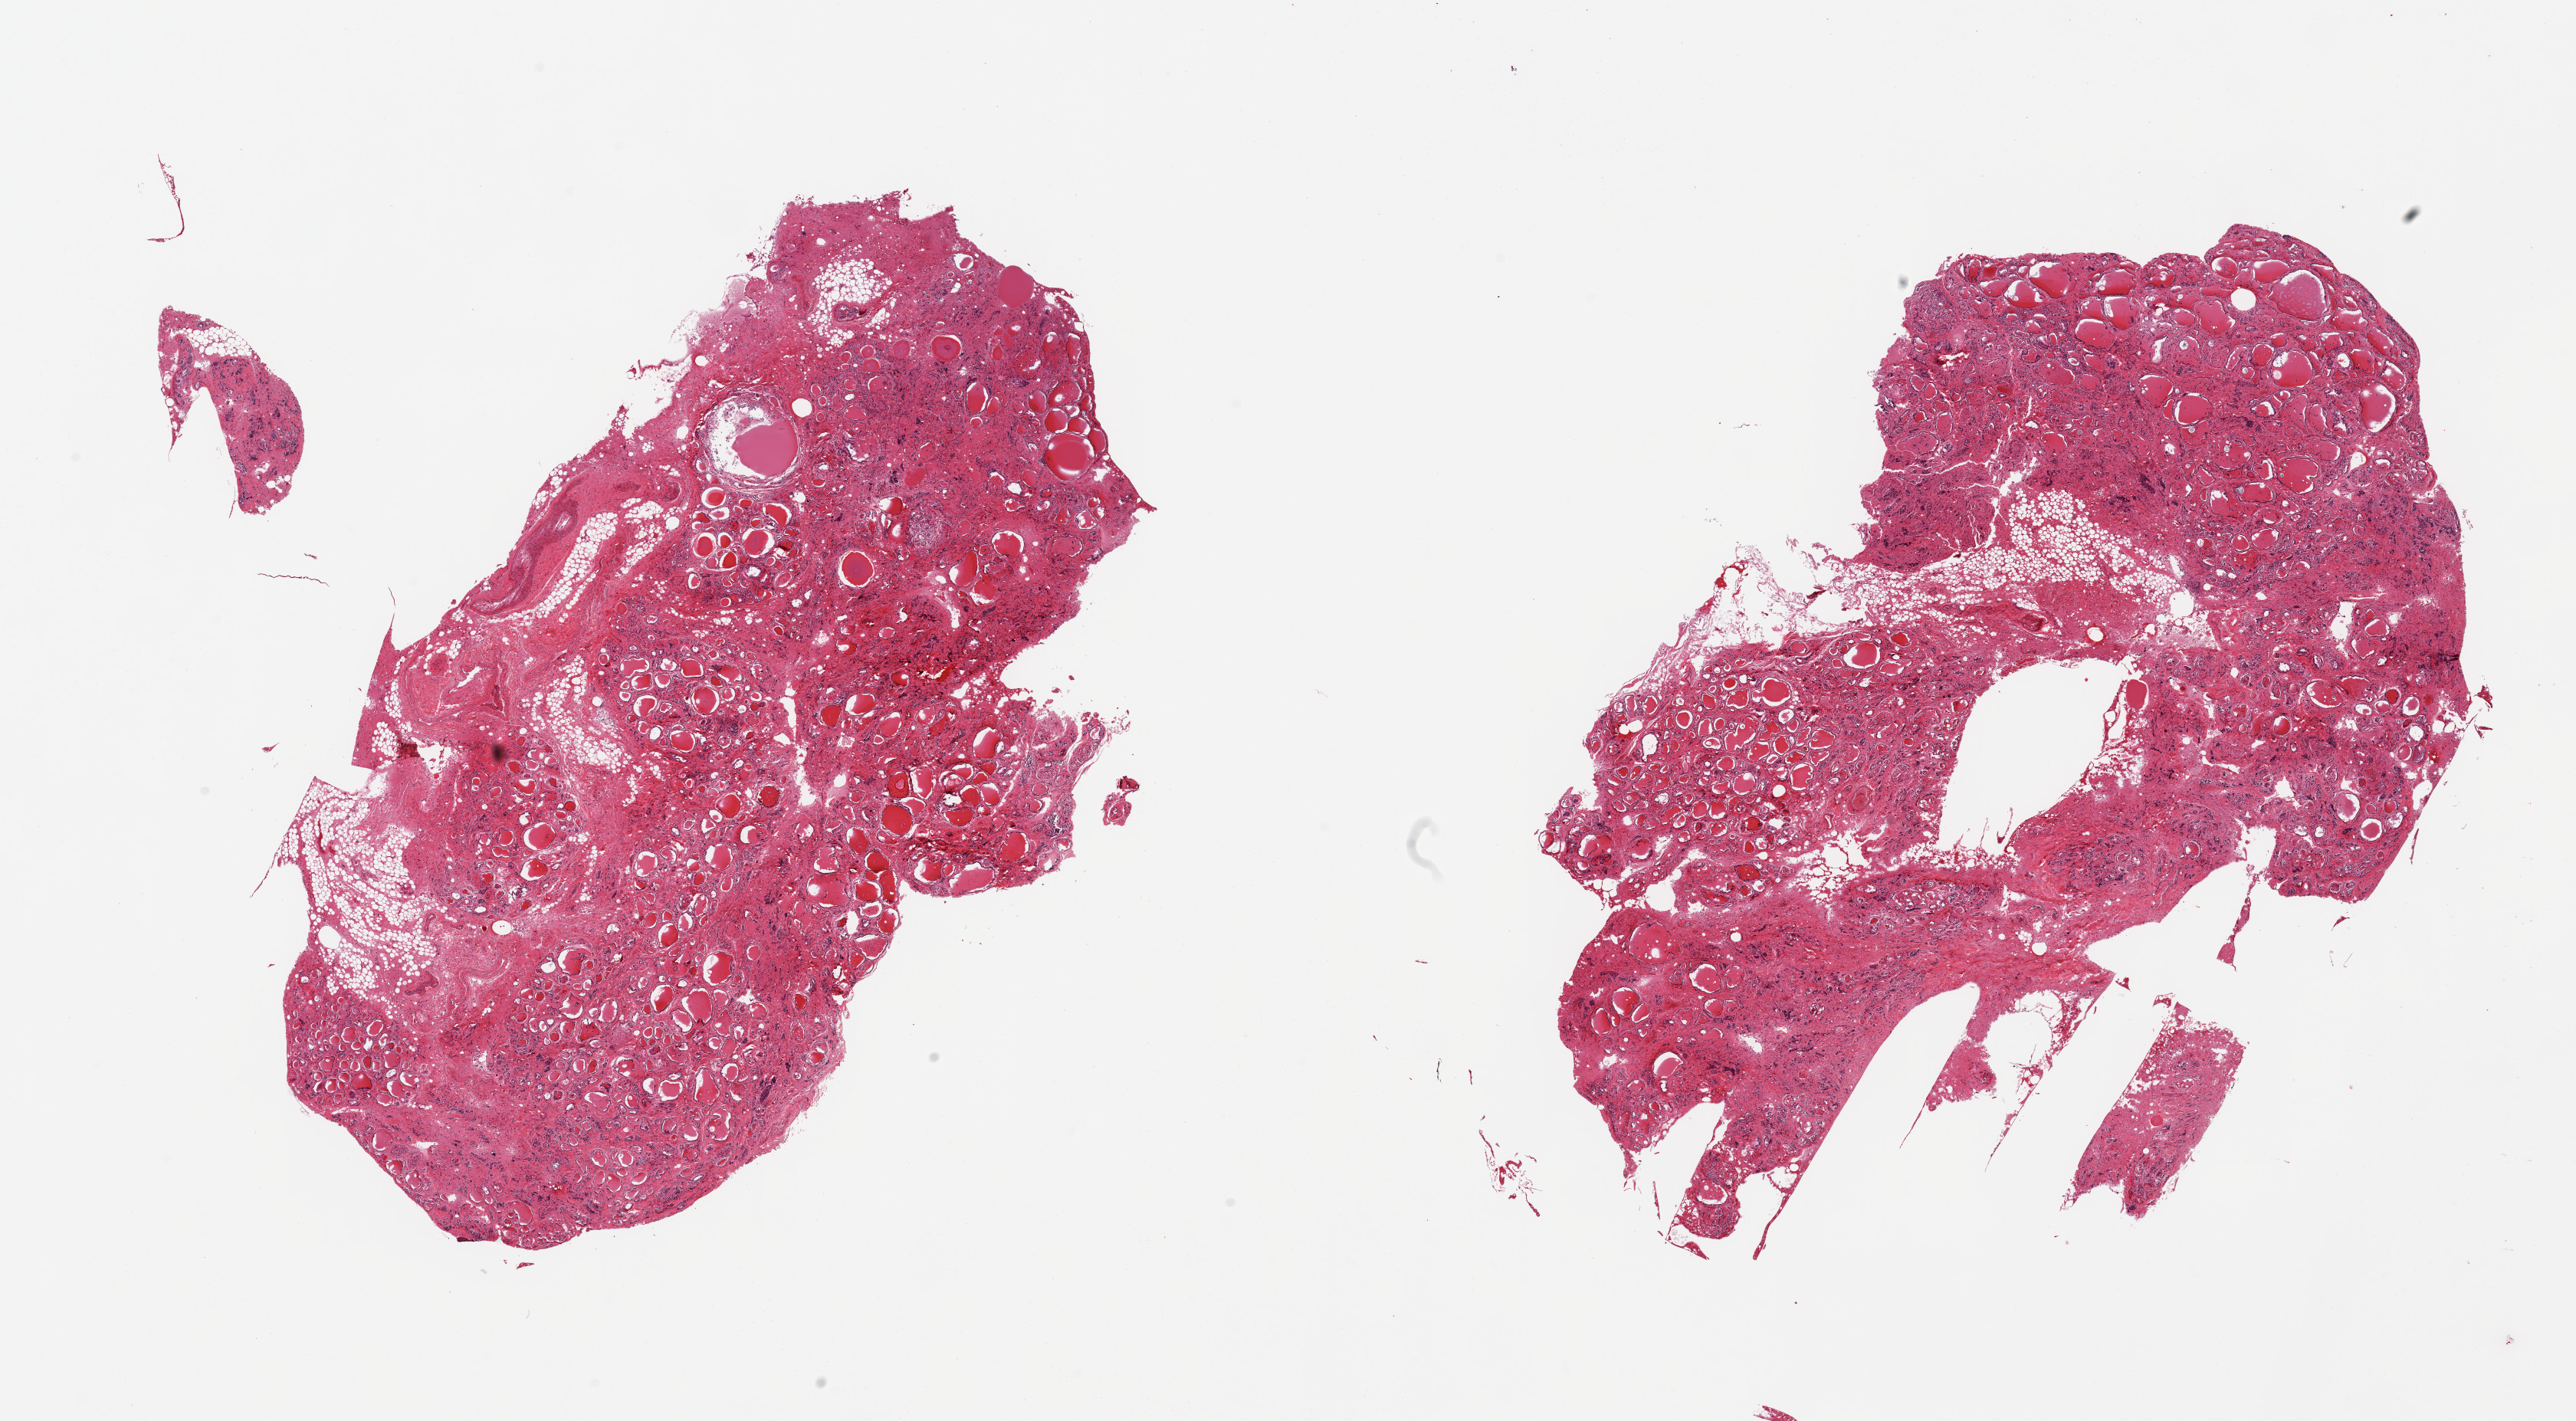
Whole-slide image, hematoxylin and eosin (H&E) stain, brightfield — shown as a low-resolution overview of the whole scanned area (about 26.6 x 14.7 mm); PAXgene-fixed paraffin-embedded (PFPE) section; target tissue: thyroid; tissue donor sample. Donor sex: male.
Pathologist's review note for this sample: 2 pieces; nodular with interstitial fibrosis with some follicuar obliteration; ~5-10% external fat.